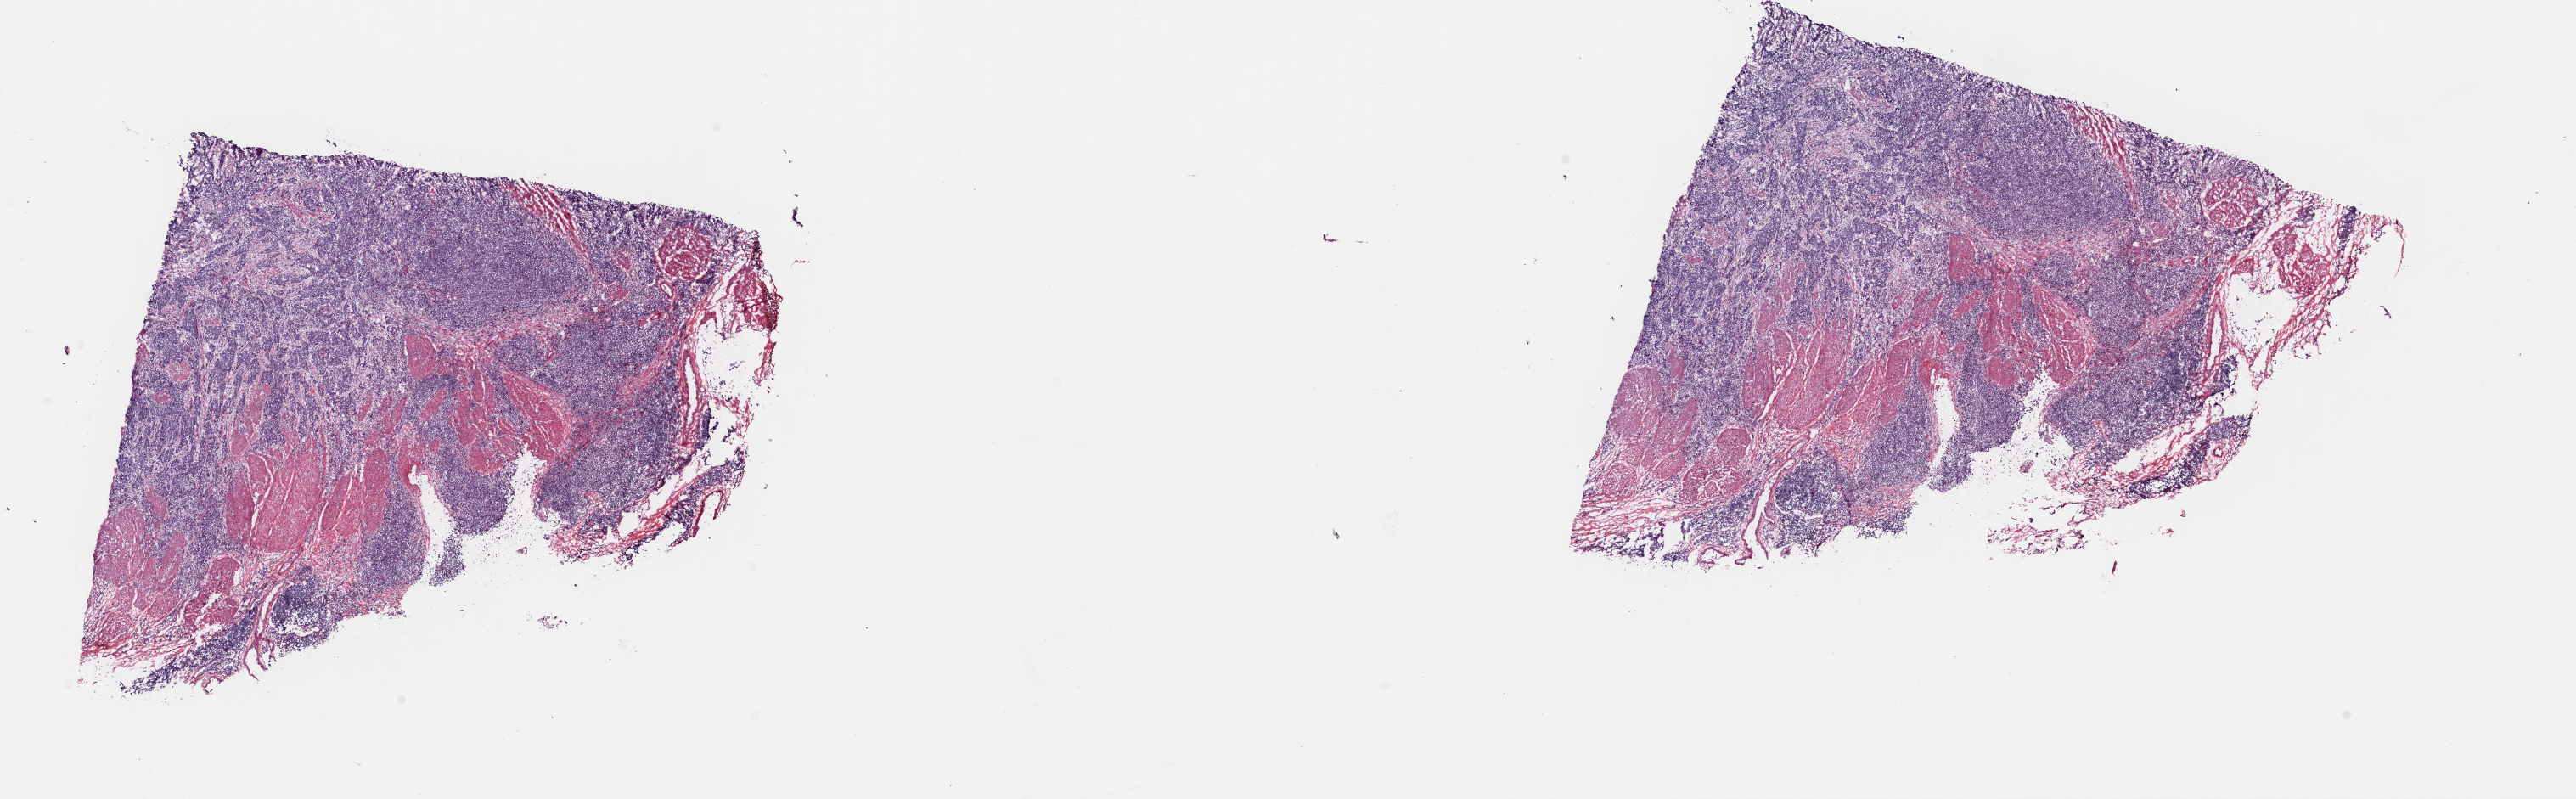
Whole-slide histology image, H&E — whole scanned area (about 24.0 x 7.4 mm, acquisition: 40x scan) shown as a low-resolution overview. Frozen section. Primary tumour sample from the bladder. Male, age 82 years at initial diagnosis. Histologic grade: high grade. Pathologist review of this section (percent, as recorded): tumour cells 60%, tumour nuclei 65%, normal cells 0%, stromal cells 39%, necrosis 1%. Inflammatory infiltration, as recorded: lymphocyte infiltration 28%, monocyte infiltration 2%, neutrophil infiltration 2%.
• AJCC pathologic stage: III (7th edition)
• histologic diagnosis: Transitional cell carcinoma (lateral wall of bladder)